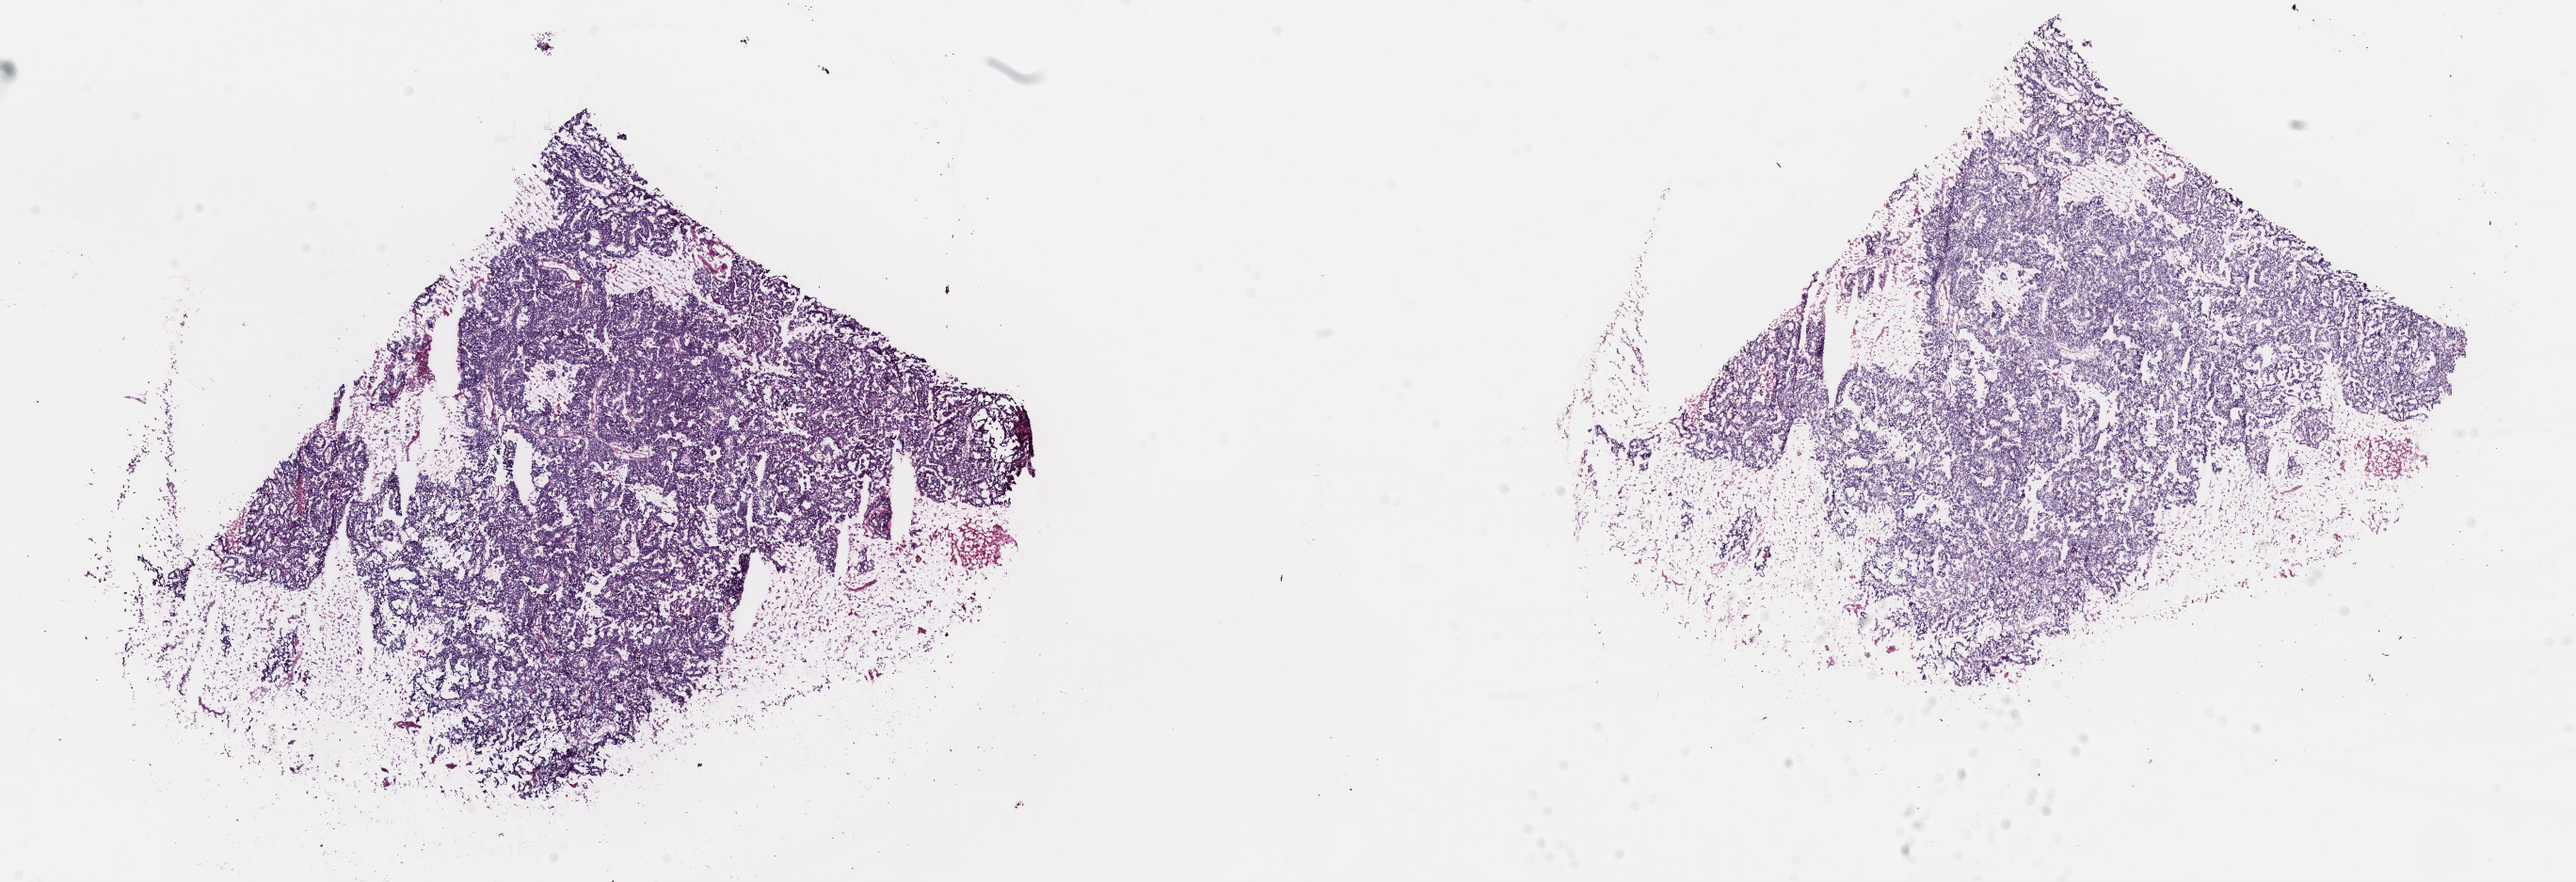
H&E whole-slide image — a low-resolution overview of the entire scanned area, about 21.6 x 7.4 mm (slide scanned at 40x). Frozen section. Uterus, primary tumour sample. Patient: female, age at initial diagnosis 66 years. Histologic grade: G3 (poorly differentiated). Pathologist review of this section (percent, as recorded): tumour cells 94%, tumour nuclei 98%, normal cells 0%, stromal cells 2%, necrosis 4%. Infiltration values recorded for this section: lymphocyte infiltration 0%, monocyte infiltration 0%, neutrophil infiltration 0%.
* FIGO stage: IIIC
* diagnosis: Serous cystadenocarcinoma, NOS (endometrium)